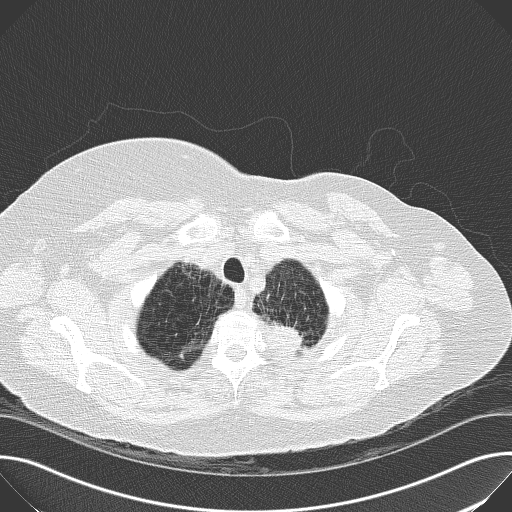
Low-dose screening chest CT, one axial slice; slice 151 of 169 in the series (ordered by position); reconstruction kernel B50f; 120 kVp; lung window (W 1500 / L -600 HU); 2 mm slice thickness; 512 × 512 image matrix.
Annotated regions visible in this slice (expert manual segmentation):
- lesion 1 (tumor, upper lobe of left lung): box from (x=275, y=323) to (x=311, y=359) px